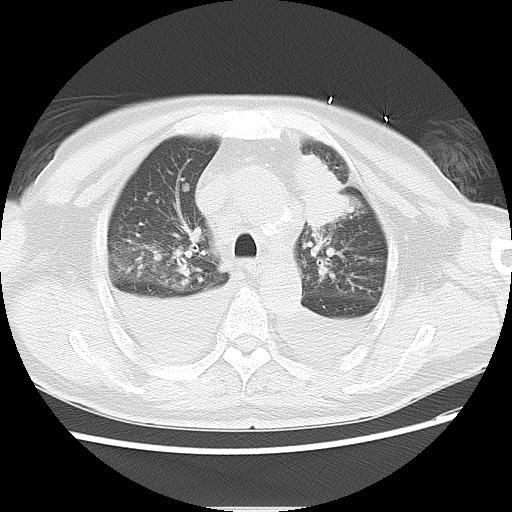
Chest CT, one axial slice; slice 19 of 22 in the series (ordered by position); reconstruction kernel LUNG; lung window (W 1500 / L -600 HU); 5 mm slice thickness; 512 × 512 image matrix, field of view 350 × 350 mm. Male patient, age 66 years. Case-level facts recorded for this patient, not image findings: clinical TNM (as recorded): T1c N0 M0.
Structures marked on this image (bounding box drawn by a radiologist):
- lung tumour (recorded histology: adenocarcinoma): bounding box (x1, y1, x2, y2) in pixels: (292, 145, 357, 227)